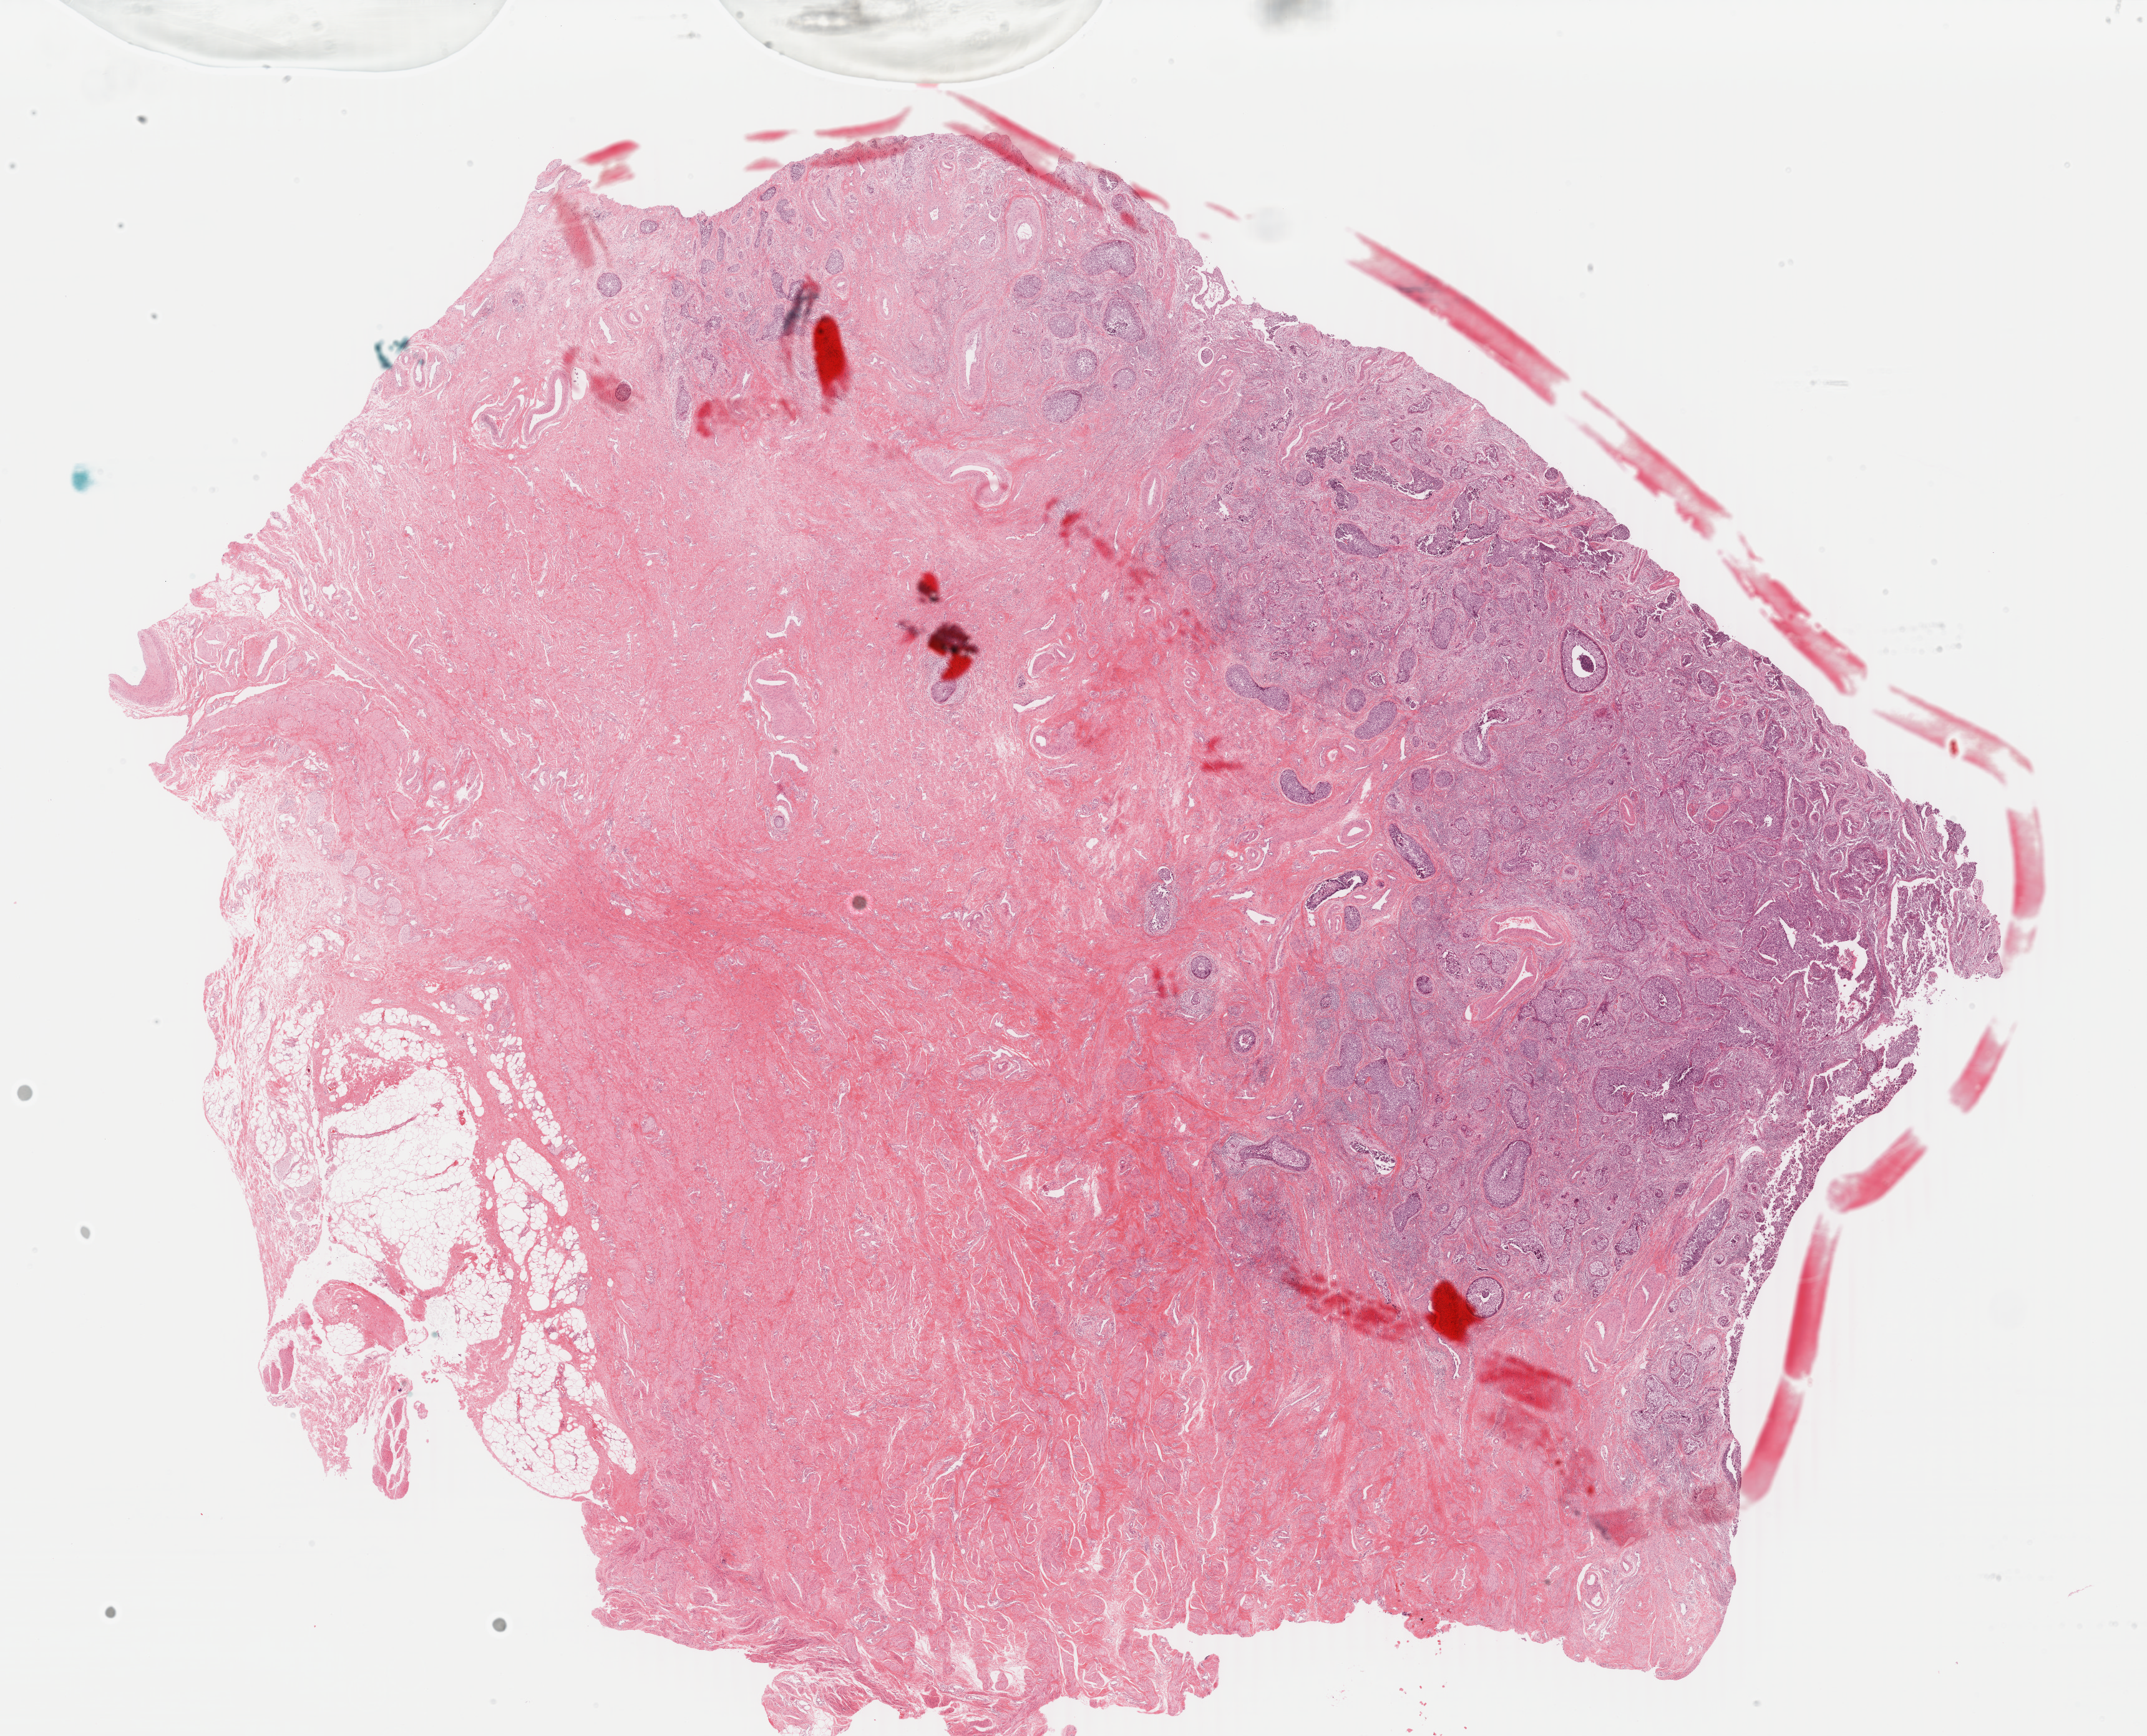
Digitized H&E tissue section (whole slide) — a low-resolution overview of the entire scanned area, about 27.4 x 22.1 mm (acquisition: 40x scan), formalin-fixed paraffin-embedded (FFPE) diagnostic section, sample: primary tumour, cervix. Female, age 50 years at initial diagnosis.
Histologic diagnosis: Squamous cell carcinoma, NOS (cervix uteri).